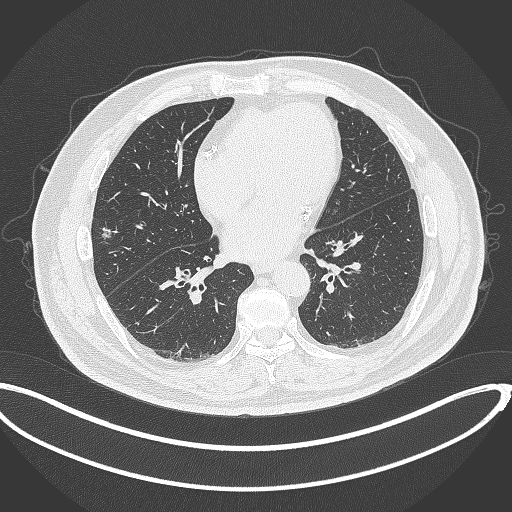
Chest CT, one axial slice; slice 135 of 340 in the series (ordered by position); 120 kVp; lung window (W 1500 / L -600 HU); 1 mm slice thickness; 512 × 512 image matrix. Male patient, age 68 years. From the clinical record (not read from this slice): clinical TNM (as recorded): T1c N0 M0.
Annotated regions visible in this slice (bounding box drawn by a radiologist):
- lung tumour (recorded histology: adenocarcinoma): bounding box <98,227,113,239> (left, top, right, bottom; pixels)